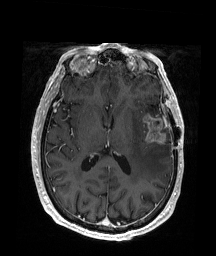
Brain MRI from a brain-tumour surgery series, one axial slice. Position 89 of 176 along the scan axis. T1-weighted post-contrast. 1 mm slice thickness. 216 × 256 image matrix, field of view 219 × 260 mm. From the clinical record (not read from this slice): histopathology: Glioblastoma; WHO grade: 4; IDH mutation: no; tumour location: Left Frontal.
Outlined on this slice (manually delineated by an expert):
- tumour: bounding box <143,113,167,145> (left, top, right, bottom; pixels)